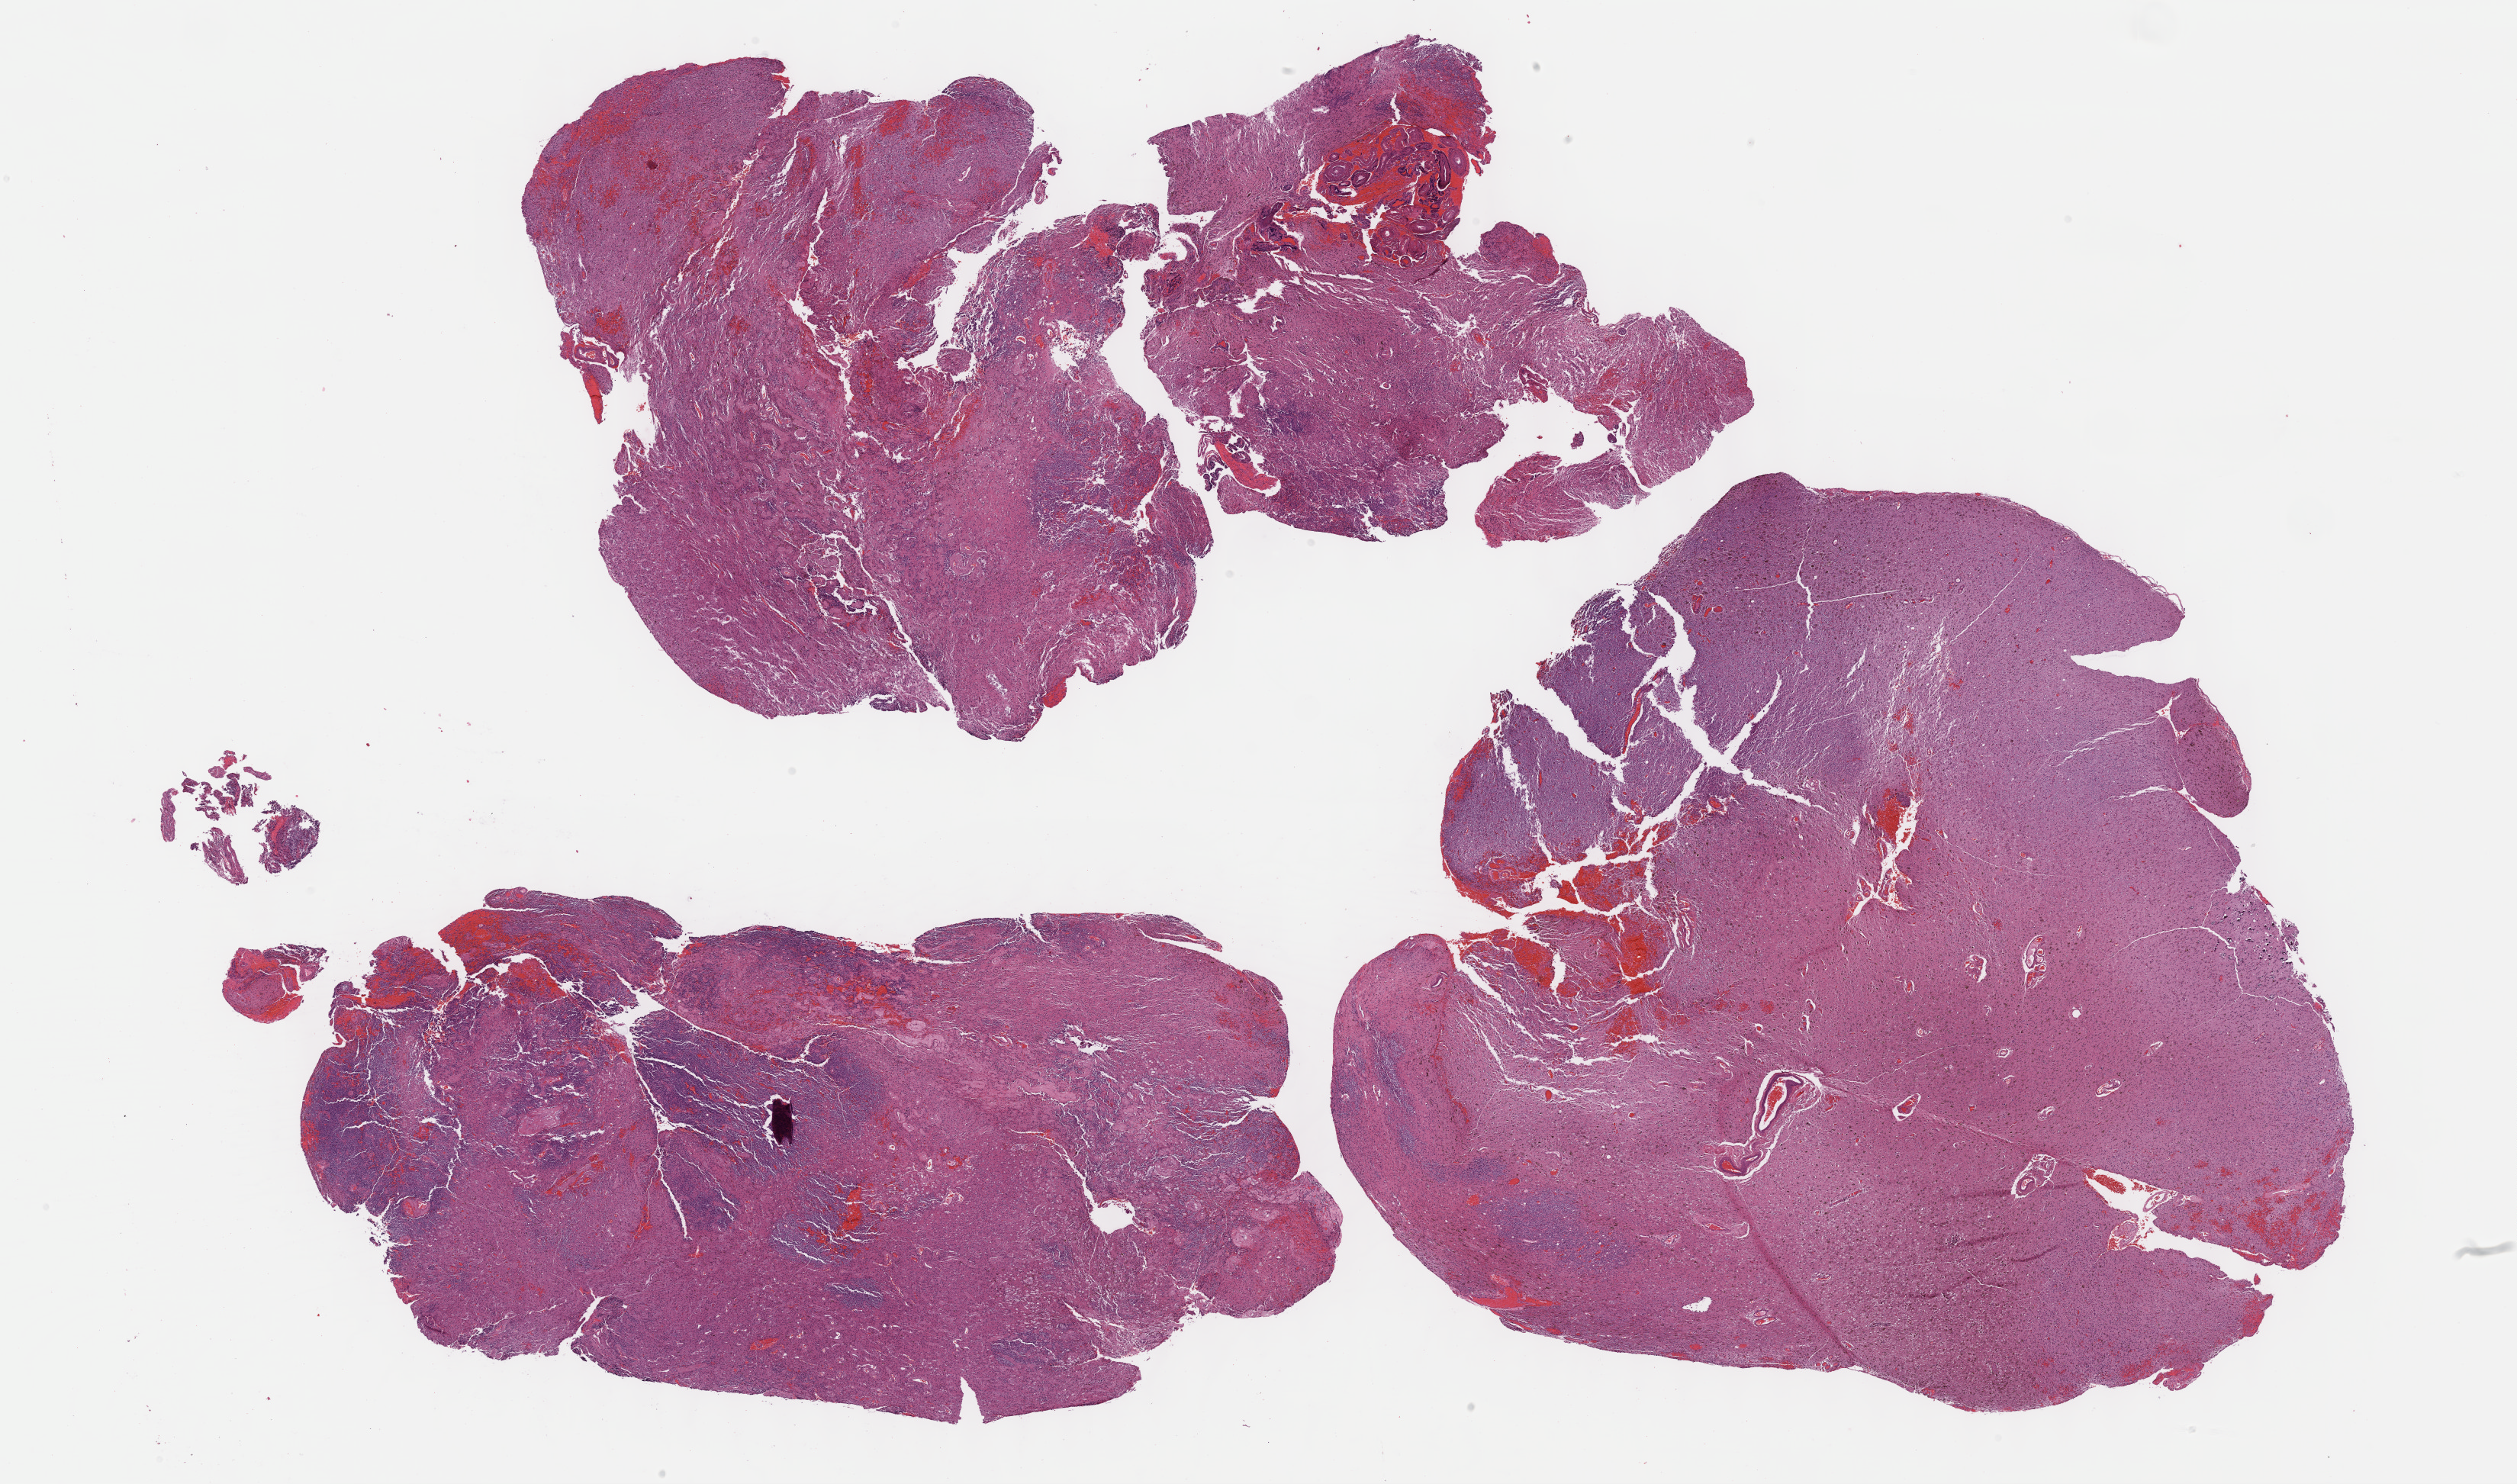
Whole-slide histology image, Hematoxylin and eosin (H&E) stained, a low-resolution overview of the entire scanned area, about 26.7 x 15.7 mm (from a 40x scan), FFPE section, sample: primary tumour, brain. Patient: male, age at initial diagnosis 75 years. Histologic grade: G3 (poorly differentiated).
• pathologic diagnosis: Oligodendroglioma, anaplastic
• laterality: right